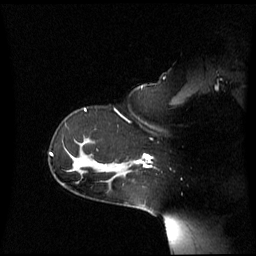
Breast MRI (dynamic contrast-enhanced), one sagittal slice; slice 46 of 60 in the series (ordered by position); dynamic contrast-enhanced series, image 2 of 3 at this slice position (ordered by acquisition); 1.5 T; TE 4.2 ms, TR 8.4 ms; 2.6 mm slice thickness; 256 × 256 image matrix. Female patient, age 39 years. From the clinical record (not read from this slice): setting: breast cancer imaged before/during neoadjuvant chemotherapy; receptor status: triple-negative.
Annotated regions visible in this slice (semi-automatic segmentation, software-assisted and operator-edited):
- analysis volume of interest (the breast-tissue region the enhancement analysis was run in; not a lesion): bounding box <117,154,152,176> (left, top, right, bottom; pixels)
- tumour enhancement mask (voxels above the 70 % enhancement threshold inside the analysis volume of interest): <132,154,152,167>